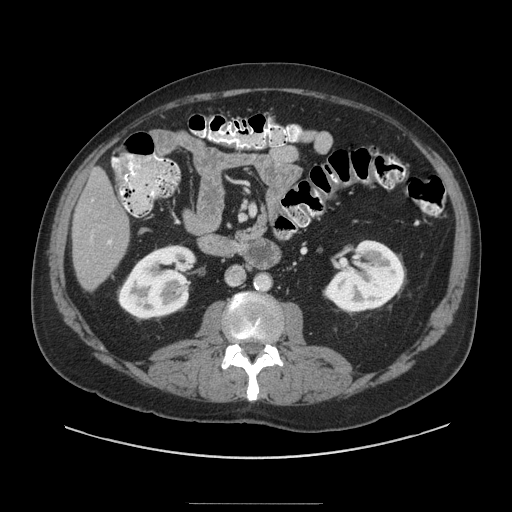
Contrast-enhanced abdominal CT (liver protocol), one axial slice; position 28 of 91 along the scan axis; reconstruction kernel STANDARD; 140 kVp; soft-tissue window (W 400 / L 40 HU); 2.5 mm slice thickness; 512 × 512 image matrix. Case-level facts recorded for this patient, not image findings: diagnosis: hepatocellular carcinoma (patient treated with transarterial chemoembolisation; whether this scan precedes or follows treatment is not stated here); TNM stage (as recorded): Stage-I.
Annotated regions visible in this slice (semi-automatically segmented with operator editing):
- liver parenchyma outside the tumour (the mass and vessels are separate outlines, so this box may not span the whole liver): bounding box <72,168,130,288> (left, top, right, bottom; pixels)
- liver vessels: <92,200,112,244>